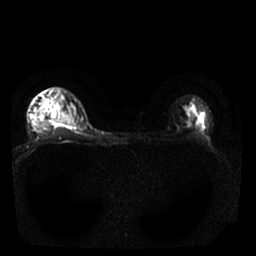
Breast MRI, one axial slice. Slice 20 of 25 in the series (ordered by position). Diffusion-weighted series; image 2 of 4 stored at this slice position (different b-values; order by instance number). 1.5 T. 256 × 256 image matrix, field of view 310 × 310 mm. Female patient.
Annotated regions visible in this slice (outlined manually by an expert reader):
- tumour on diffusion-weighted imaging: bounding box <51,113,56,119> (left, top, right, bottom; pixels)